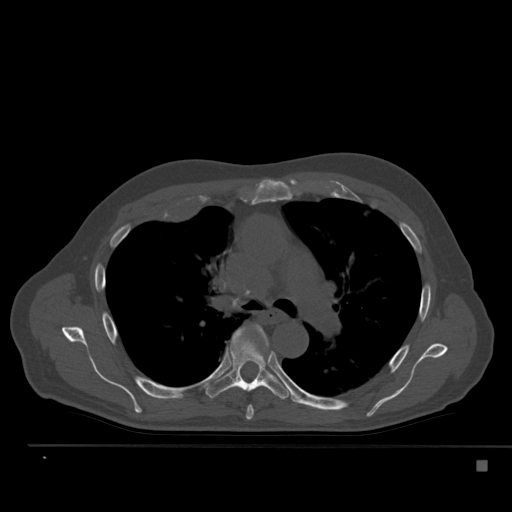
CT including the spine, one axial slice; slice 353 of 517 in the series (ordered by position); reconstruction kernel Br40s; bone window (W 1800 / L 400 HU); 512 × 512 image matrix. Male patient, age 70 years. Case-level facts recorded for this patient, not image findings: primary cancer: renal.
Annotated regions visible in this slice (semi-automatic segmentation, software-assisted and operator-edited):
- T5 vertebra: bounding box [x1, y1, x2, y2] px = [246, 351, 271, 420]
- T6 vertebra: [206, 327, 291, 400]